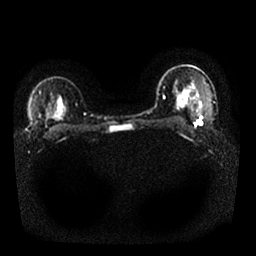
Breast MRI, one axial slice; slice 18 of 25 in the series (ordered by position); diffusion-weighted series; image 2 of 4 stored at this slice position (different b-values; order by instance number); 1.5 T; 256 × 256 image matrix, field of view 340 × 340 mm. Female patient.
Outlined on this slice (manually delineated by an expert):
- tumour on diffusion-weighted imaging: bounding box [x1, y1, x2, y2] px = [195, 116, 203, 125]